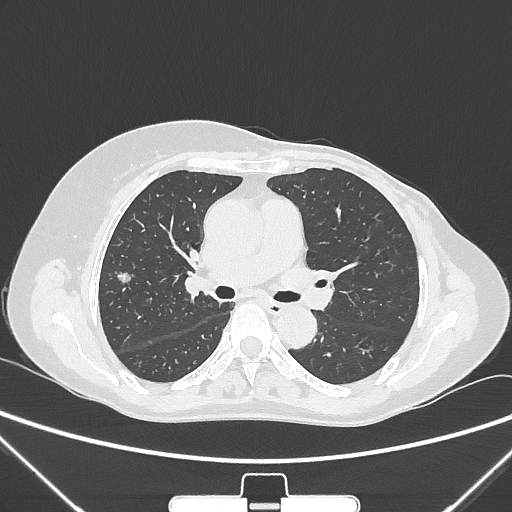
Chest CT, one axial slice. 120 kVp. Lung window (W 1500 / L -600 HU). 1 mm slice thickness. 512 × 512 image matrix. Patient: female, 64 years. Case-level facts recorded for this patient, not image findings: clinical TNM (as recorded): T1c N0 M0.
Annotated regions visible in this slice (rectangle marked by the reading radiologist):
- lung tumour (recorded histology: adenocarcinoma): bounding box [x1, y1, x2, y2] px = [109, 267, 134, 289]